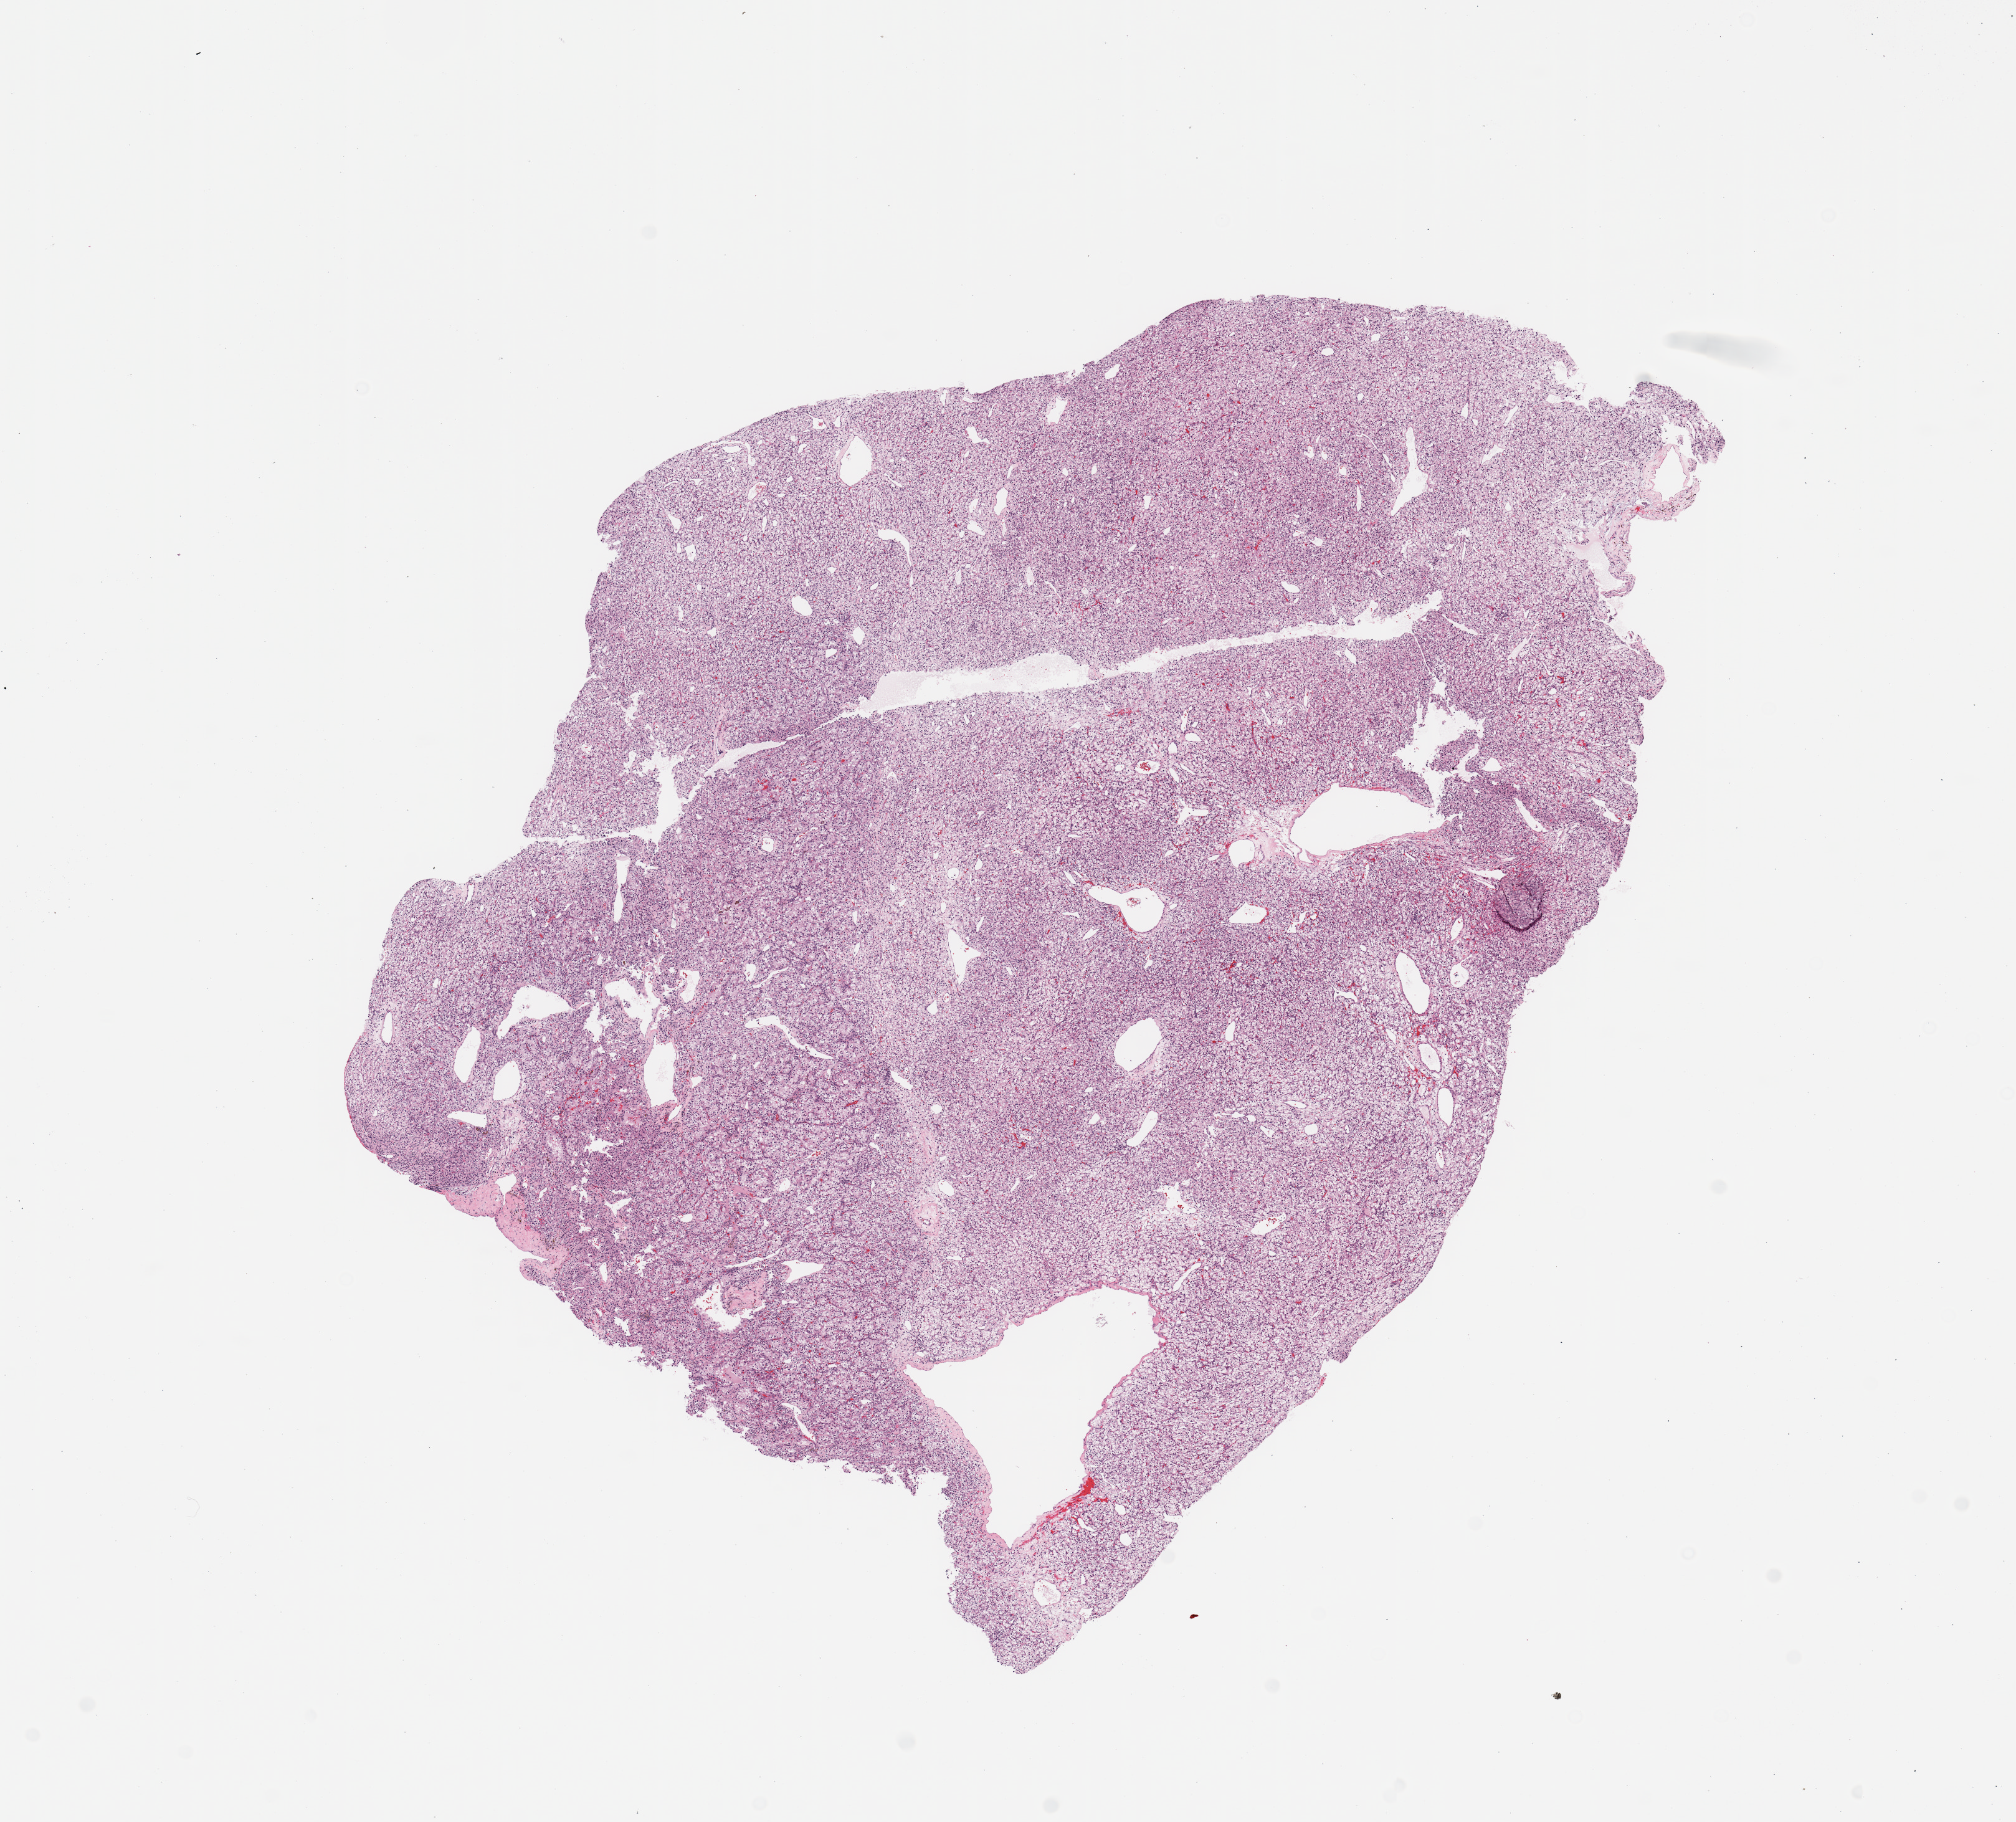
Digitized H&E-stained tissue section (whole slide) — shown as a low-resolution overview of the whole scanned area (about 12.8 x 11.6 mm, slide scanned at 20x). Tumour tissue sample, sampled site: kidney. Male, 72 y/o. Histologic grade: G3 (poorly differentiated). Composition of this section per pathologist review: tumour nuclei 85%, necrosis 0%.
Diagnosis: Renal cell carcinoma, NOS. AJCC pathologic stage: III. Primary tumour site (as recorded): lower pole.